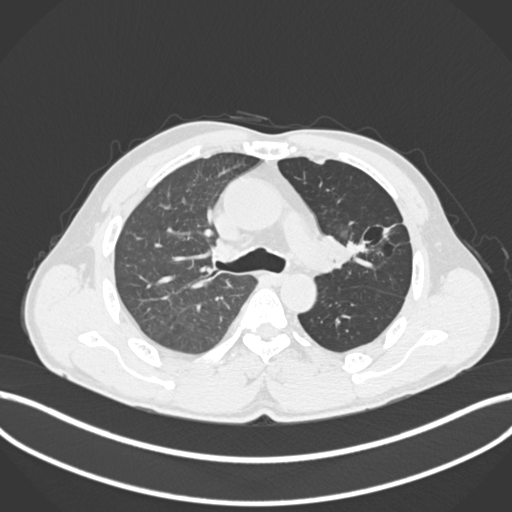
Chest CT, one axial slice. Slice 127 of 255 in the series (ordered by position). Lung window (W 1500 / L -600 HU). 512 × 512 image matrix, field of view 400 × 400 mm. Patient: male, 57 years. Case-level facts recorded for this patient, not image findings: clinical TNM (as recorded): T2b N0 M0.
Outlined on this slice (rectangle marked by the reading radiologist):
- lung tumour (recorded histology: squamous cell carcinoma): box from (x=315, y=225) to (x=371, y=272) px